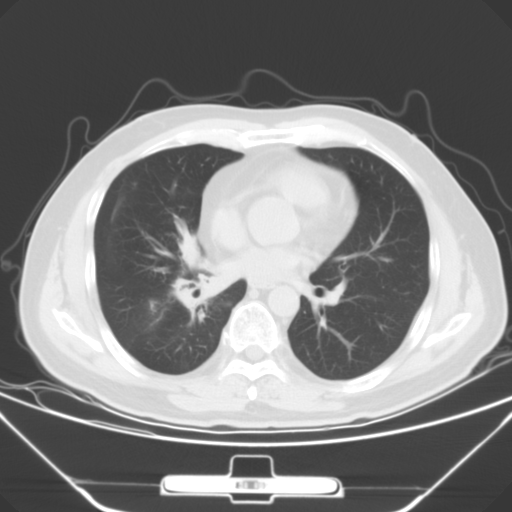
Chest CT, one axial slice. Position 26 of 56 along the scan axis. 120 kVp. Lung window (W 1500 / L -600 HU). 5 mm slice thickness. 512 × 512 image matrix. Male patient, age 48 years. From the clinical record (not read from this slice): clinical TNM (as recorded): T1a N1 M1c.
Outlined on this slice (rectangle marked by the reading radiologist):
- lung tumour (recorded histology: adenocarcinoma): bounding box (x1, y1, x2, y2) in pixels: (169, 224, 222, 315)